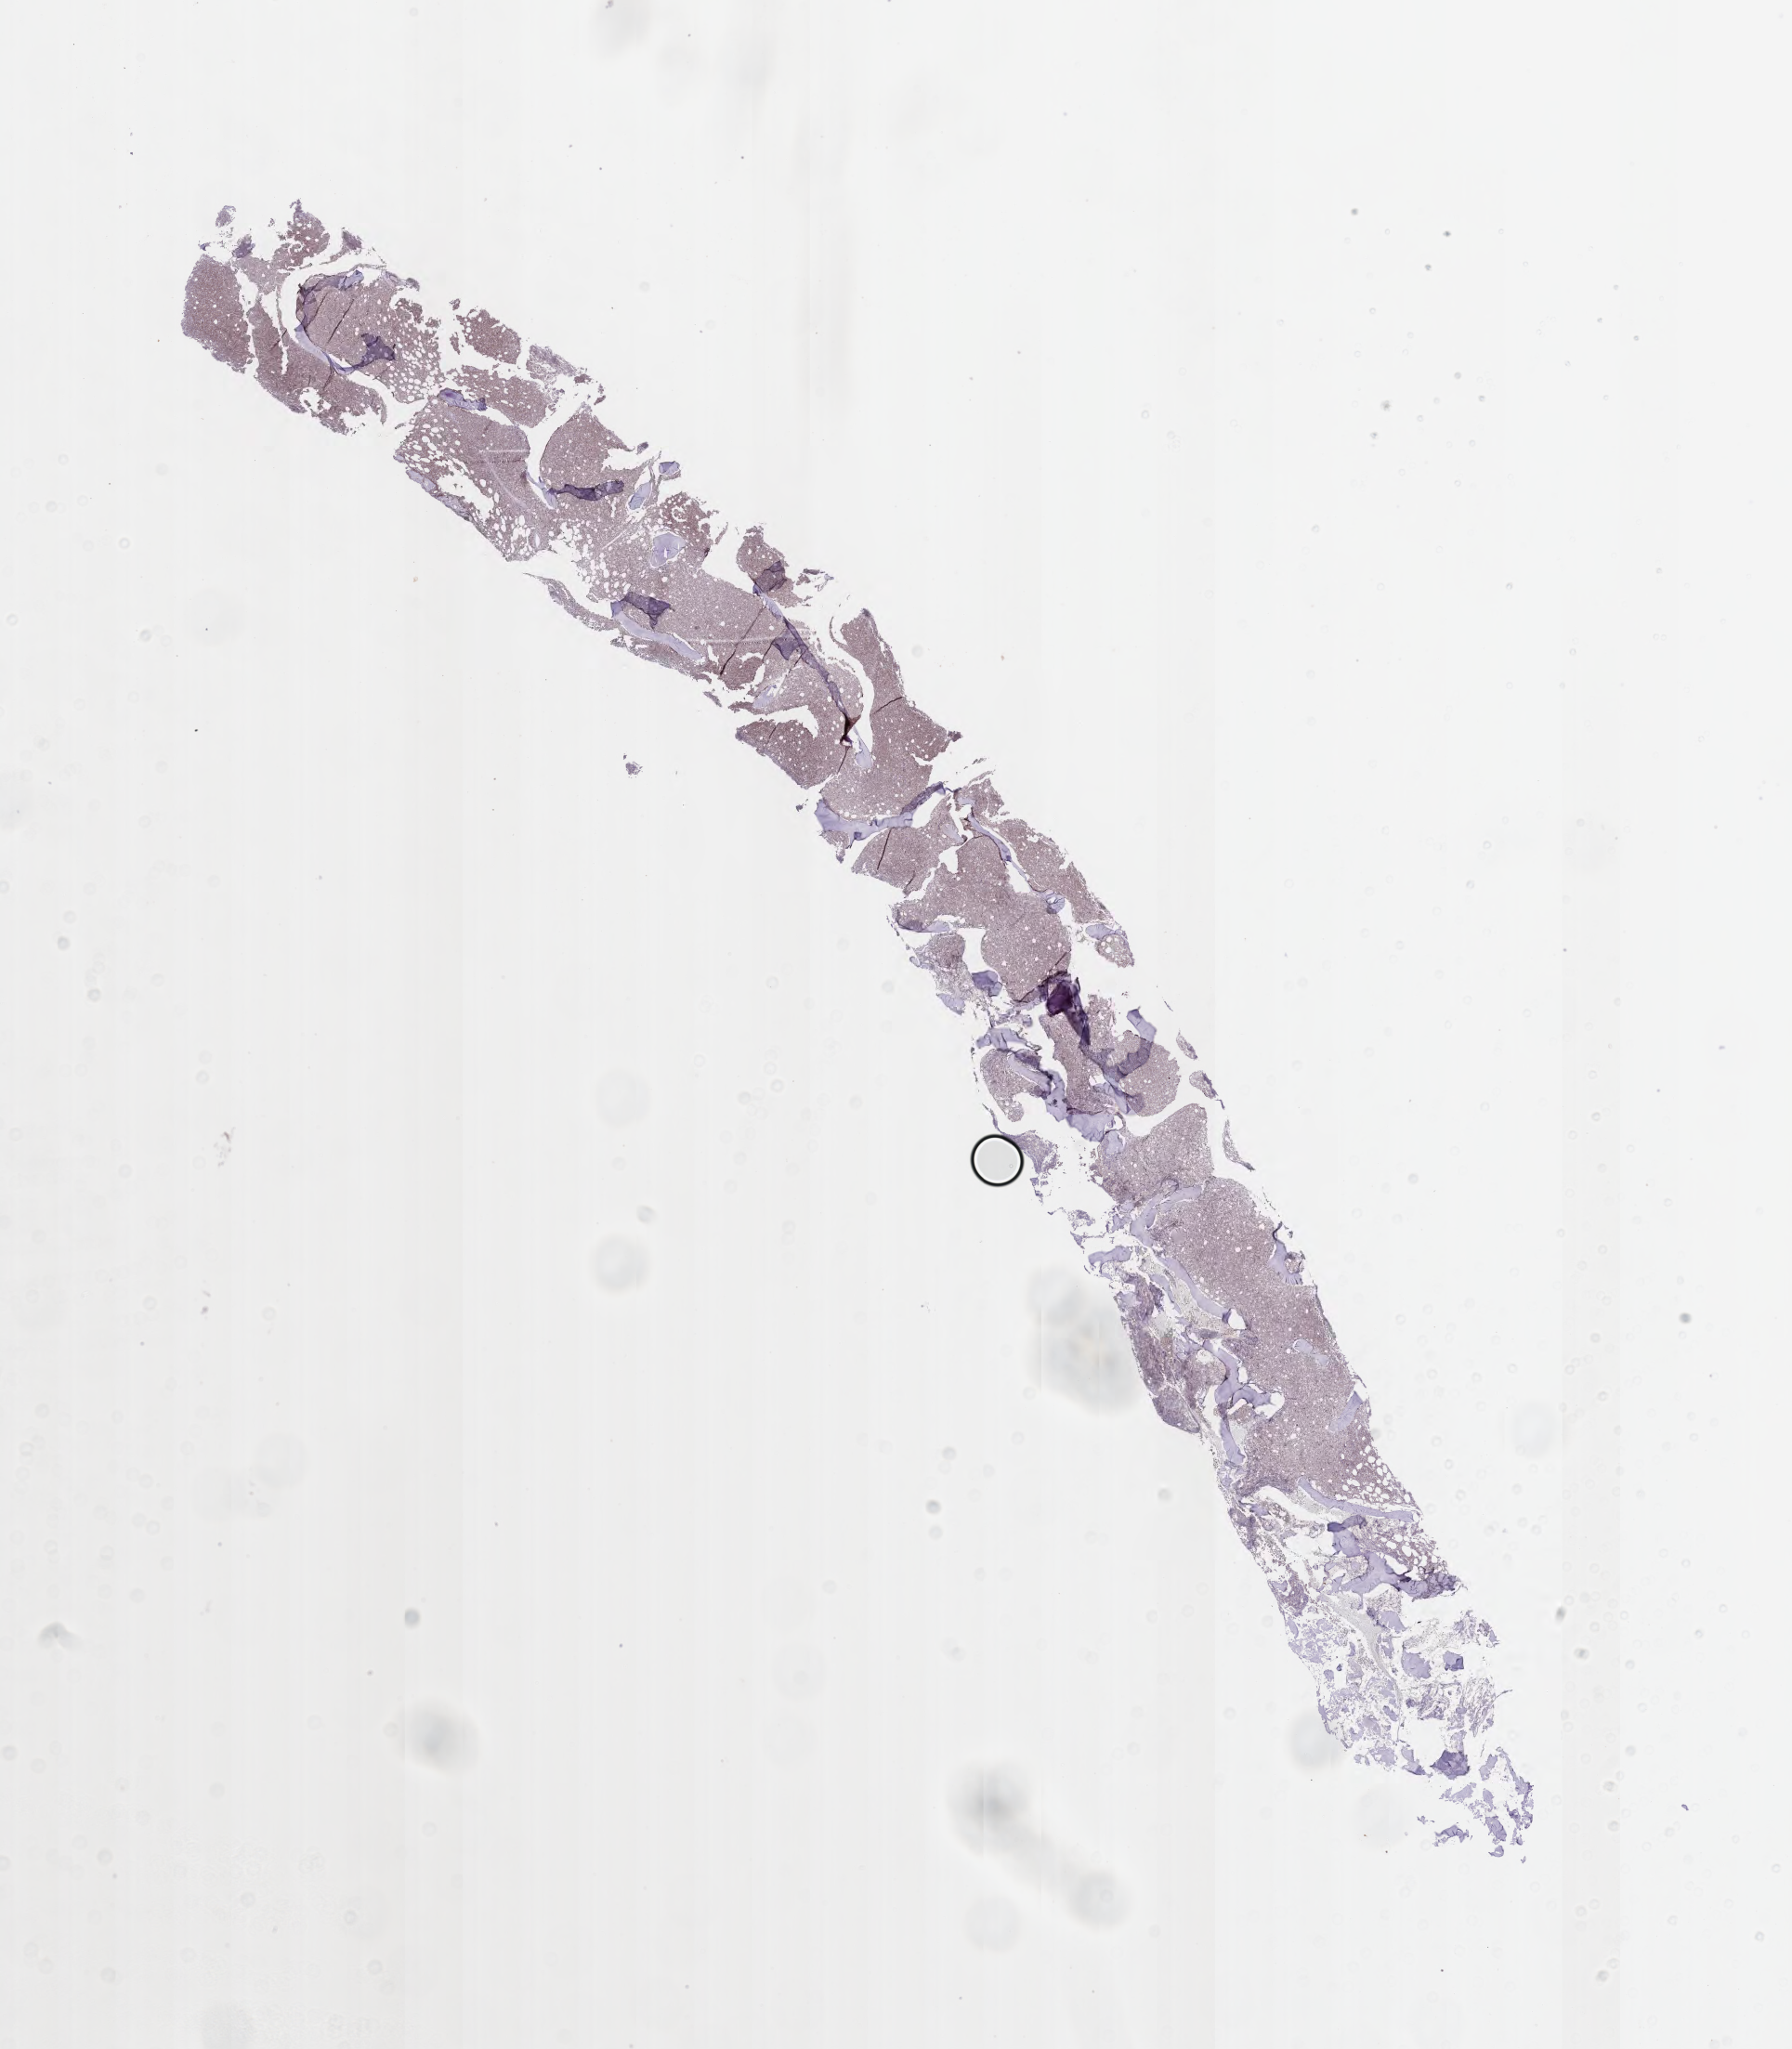
Immunohistochemistry (IHC) whole-slide image stained for BCL6 — a low-resolution overview of the entire scanned area, about 15.6 x 17.8 mm. Tumor tissue. Male patient.
Histologic diagnosis: Burkitt lymphoma, NOS.